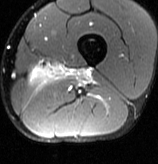
MRI of an extremity soft-tissue mass, one axial slice. Slice 19 of 70 in the series (ordered by position). T2-weighted fat-saturated. MR volume resampled by the dataset authors to the PET/CT grid (not the native acquisition matrix). 3.27 mm slice thickness. 158 × 164 image matrix. Male patient. From the clinical record (not read from this slice): histological type: extraskeletal osteosarcoma; grade: high; site of the primary tumour: left adductur.
Annotated regions visible in this slice (expert contour drawn on MRI and transferred to this co-registered scan by the dataset authors):
- gross tumour volume (mass): bounding box <29,66,93,90> (left, top, right, bottom; pixels)